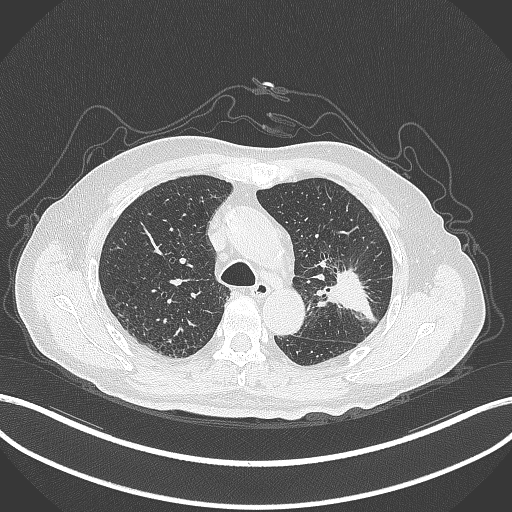
Chest CT, one axial slice; slice 202 of 331 in the series (ordered by position); reconstruction kernel B70f; lung window (W 1500 / L -600 HU); 1 mm slice thickness; 512 × 512 image matrix, field of view 400 × 400 mm. Patient: male, 79 years. From the clinical record (not read from this slice): clinical TNM (as recorded): T2a N1 M1; histopathological grade: G3.
Outlined on this slice (rectangle marked by the reading radiologist):
- lung tumour (recorded histology: adenocarcinoma): bounding box [x1, y1, x2, y2] px = [318, 264, 377, 326]